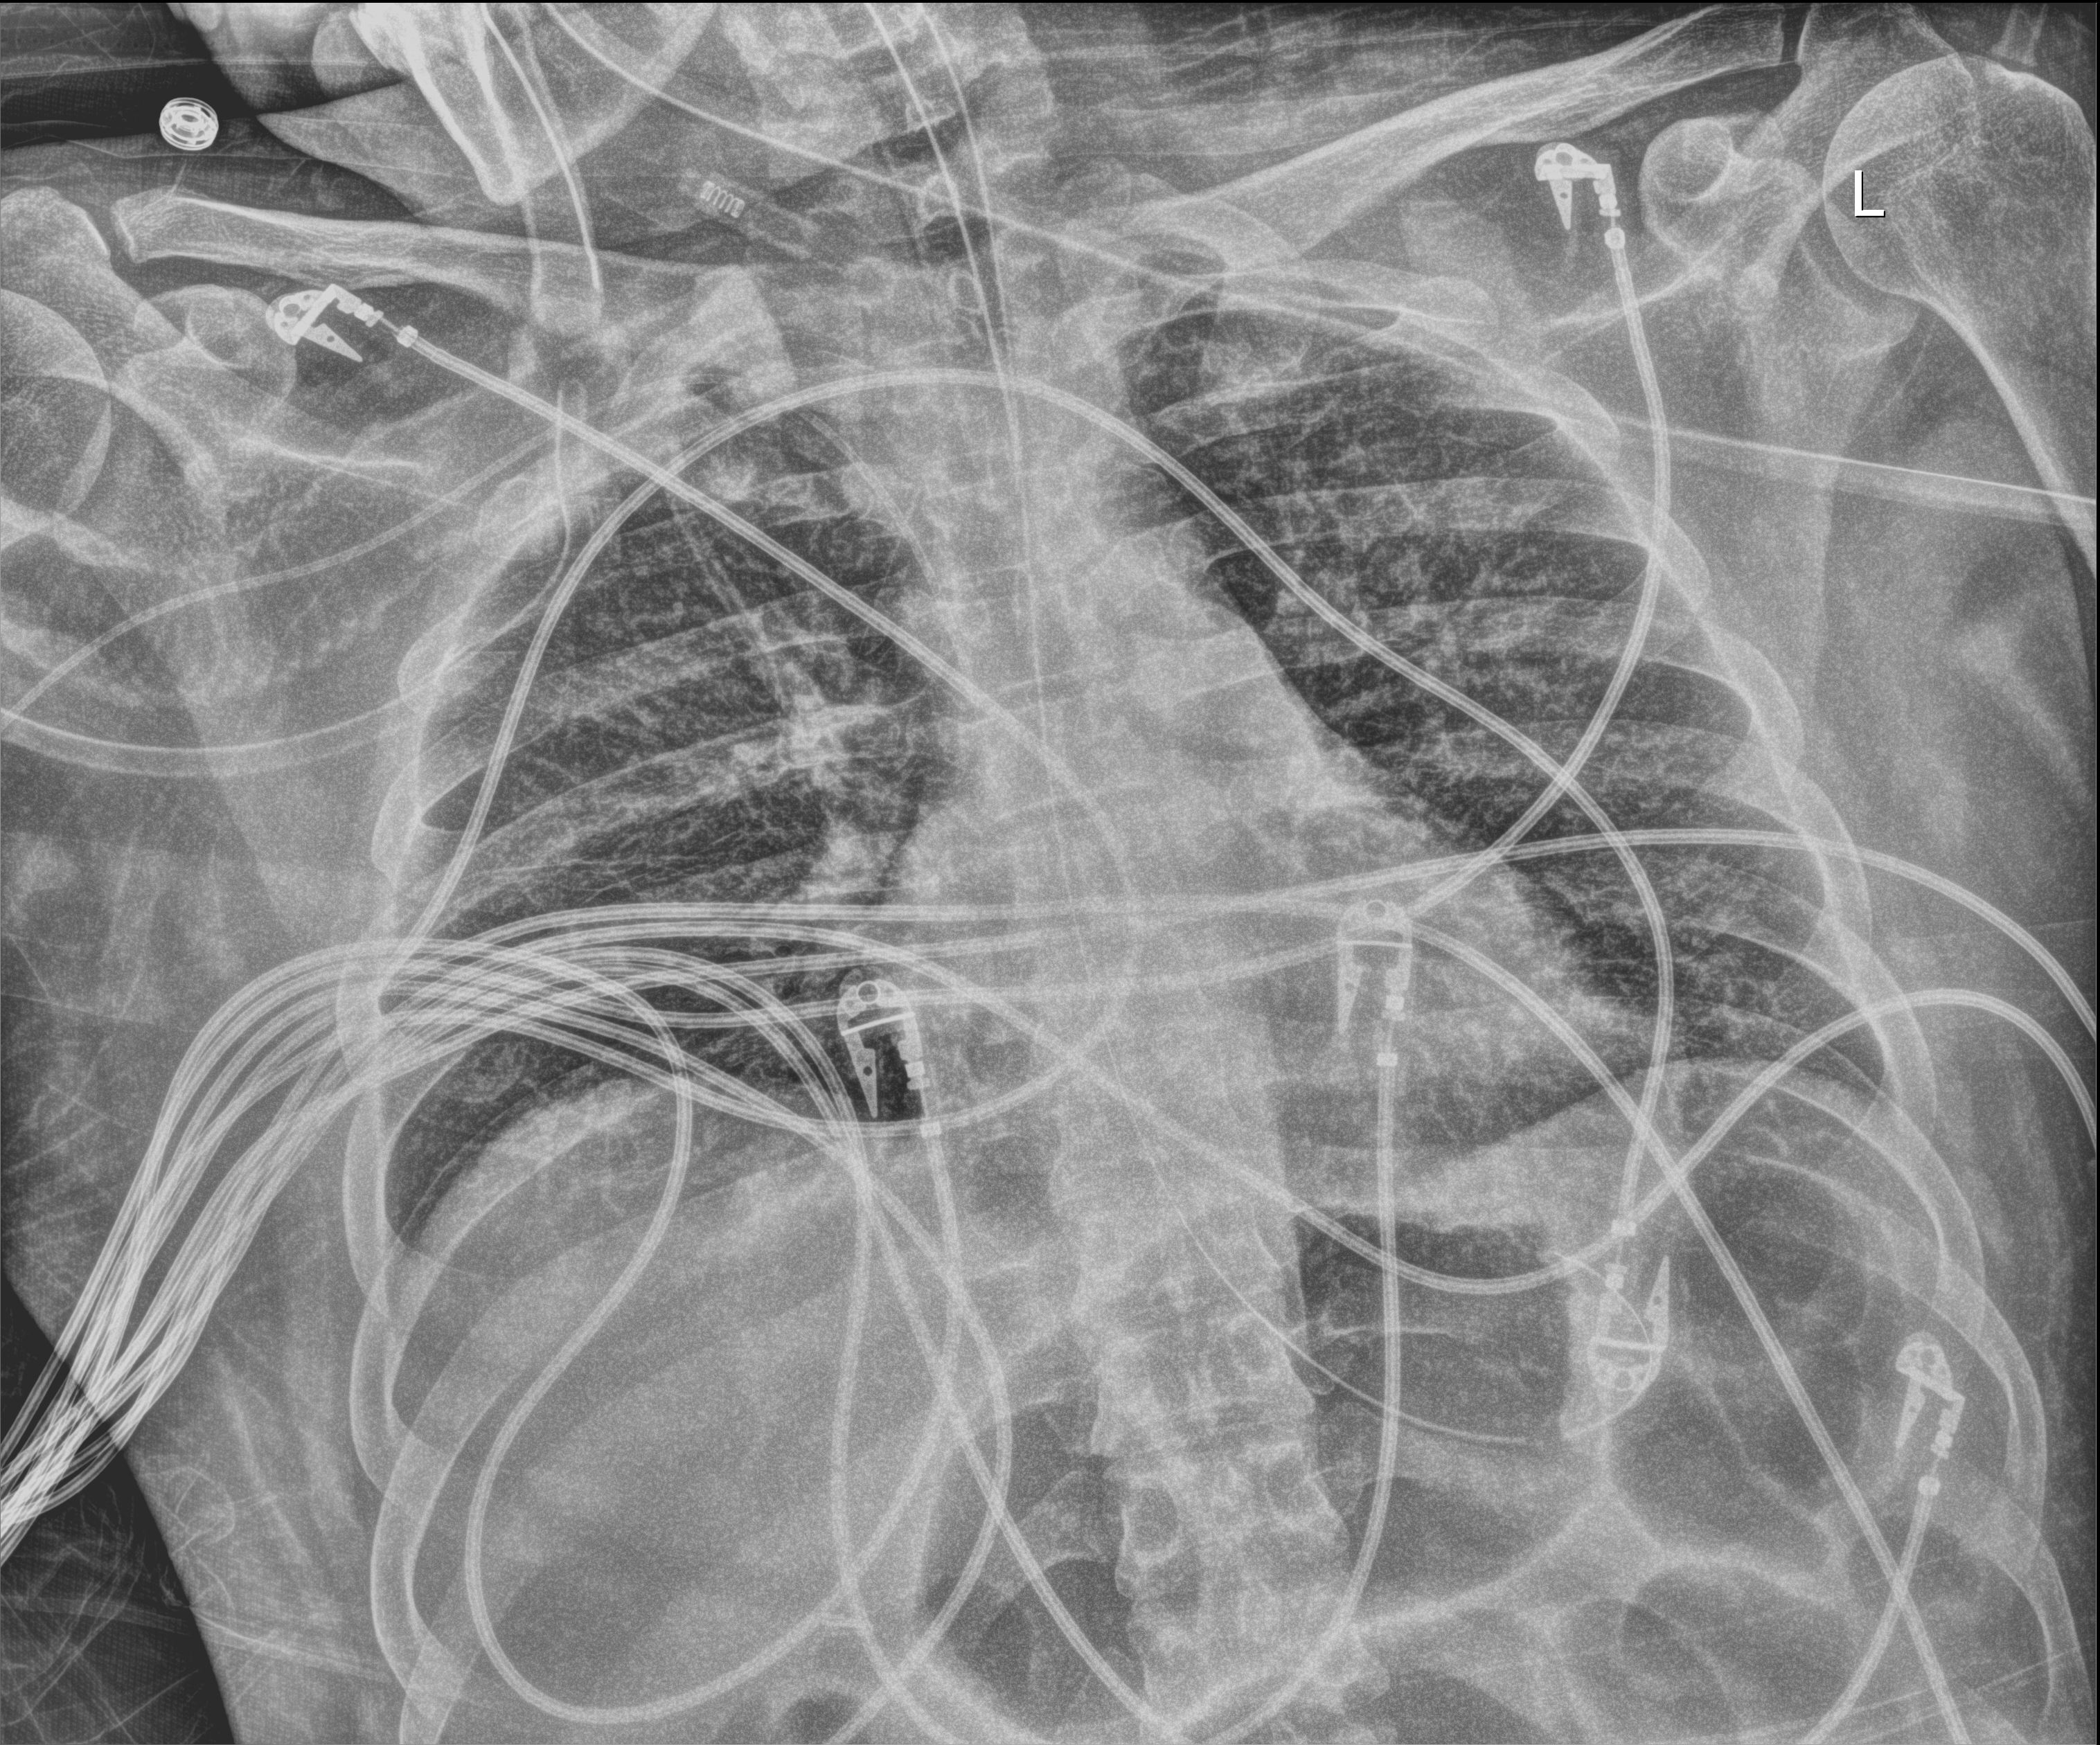
Bedside chest radiograph (digital radiography), anteroposterior (AP) projection. Patient hospitalised with COVID-19; male, aged 18–59 years.
Hospital-stay facts (about this admission, not read from this image; timing relative to this image not recorded): diabetes (admission record): yes; chronic kidney disease (admission record): no.